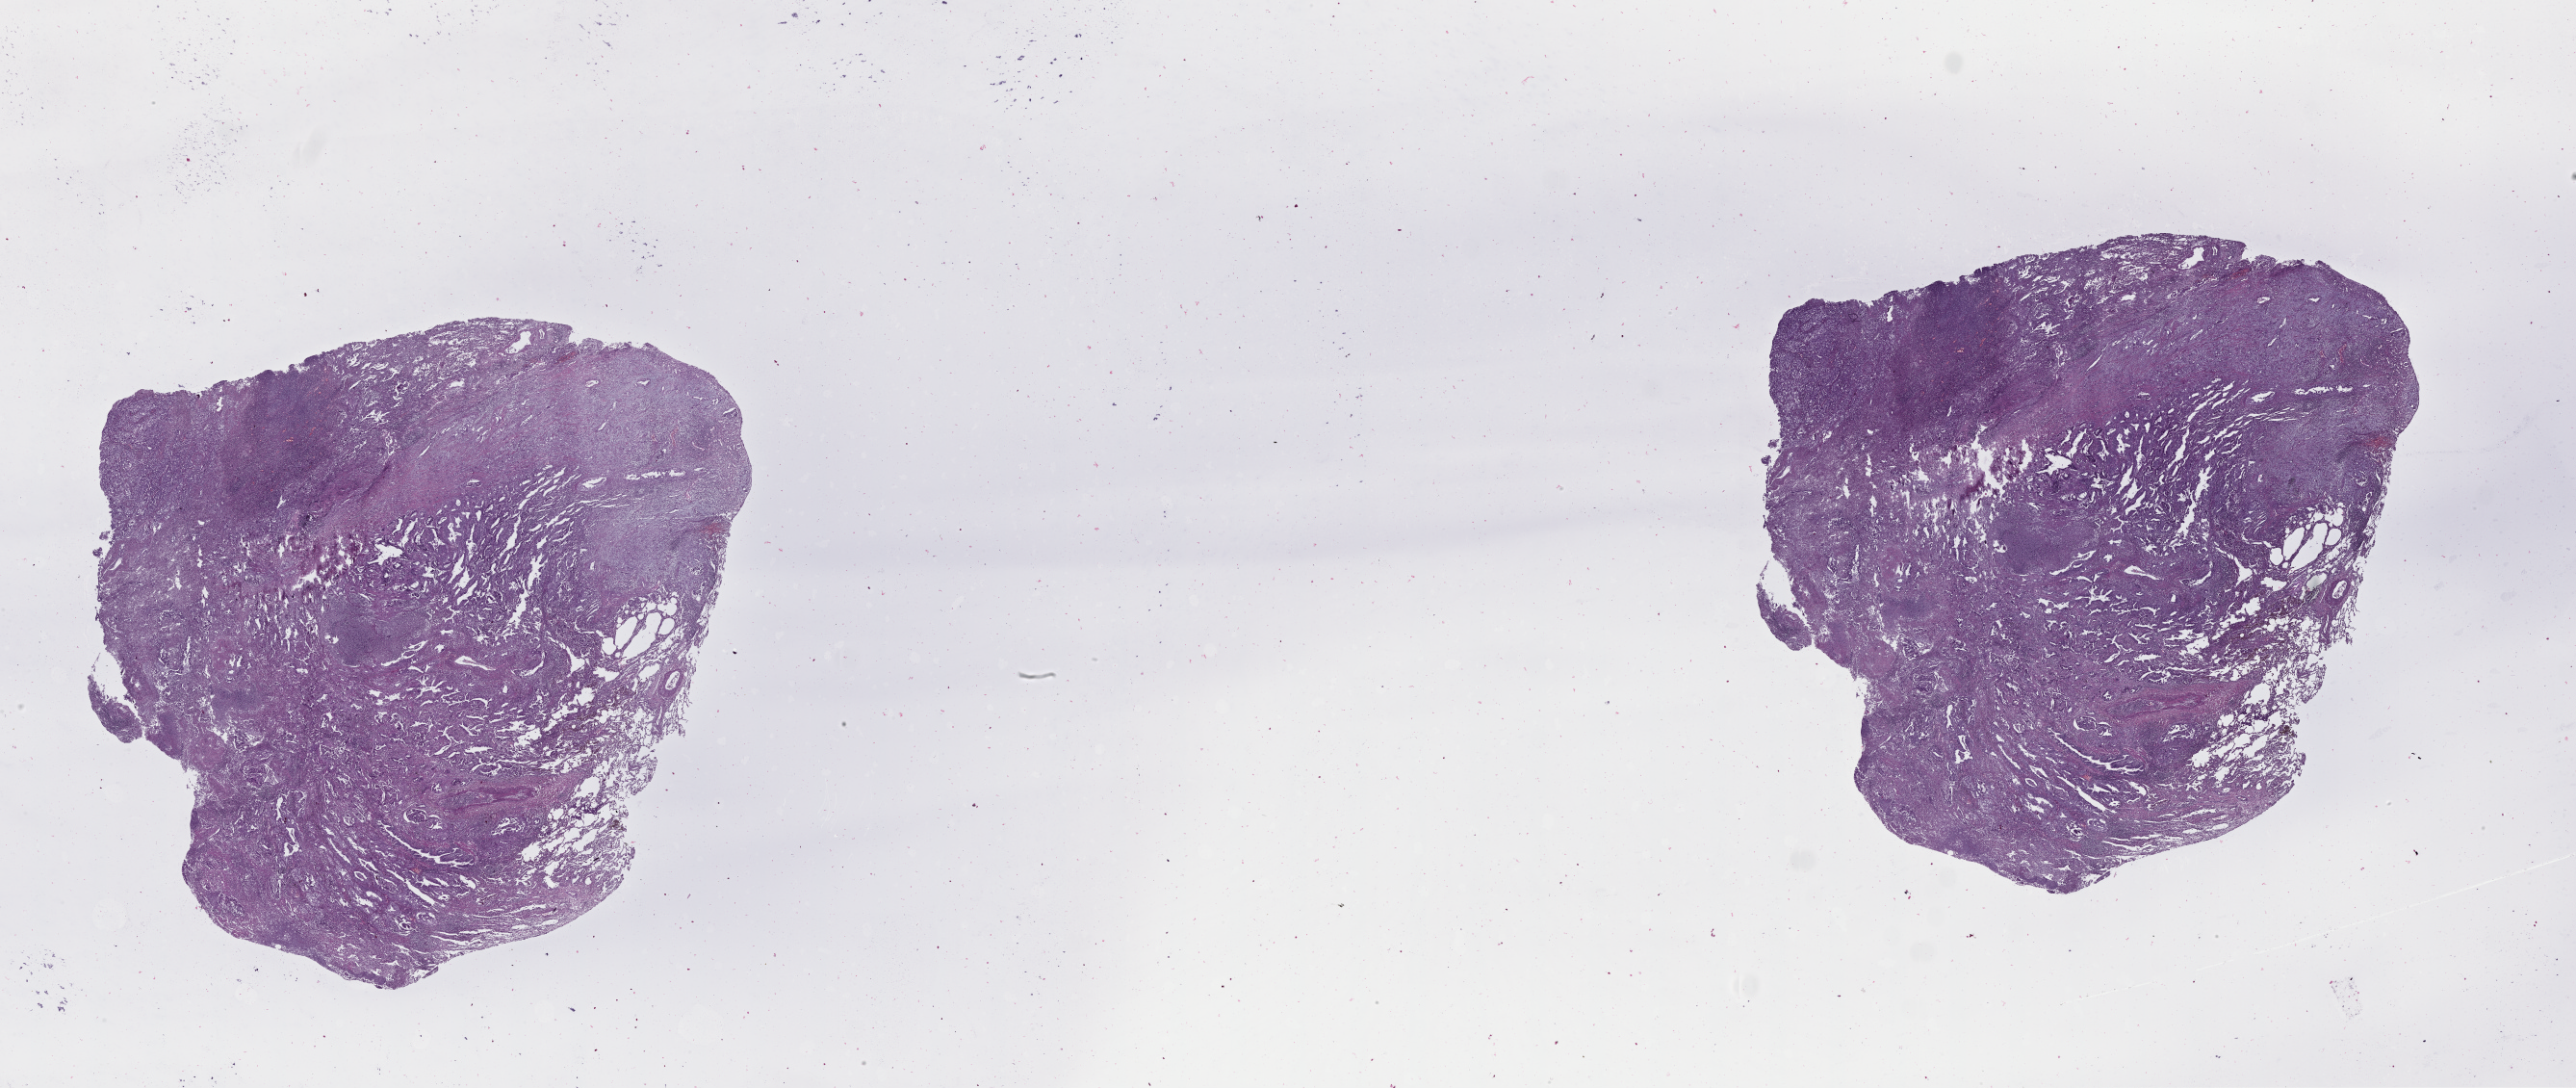
H&E whole-slide image — whole scanned area (about 43.1 x 18.2 mm, slide scanned at 20x) shown as a low-resolution overview. Lung, tissue type not recorded.
* patient diagnosis (cohort enrolment): lung adenocarcinoma (lung)